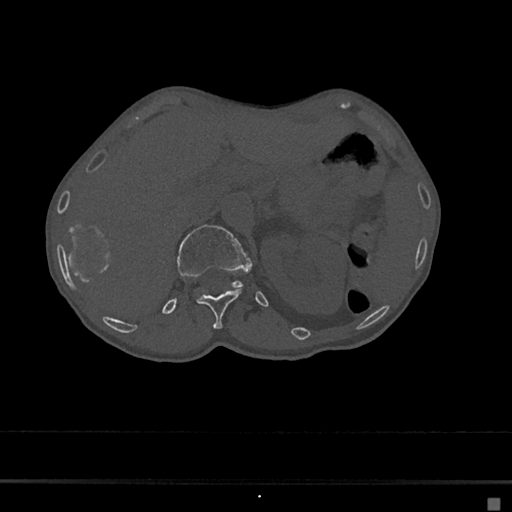
CT including the spine, one axial slice; reconstruction kernel Br40s/3; 120 kVp; bone window (W 1800 / L 400 HU); 0.5 mm slice thickness; 512 × 512 image matrix, field of view 360 × 360 mm. Patient: female, 68 years. Case-level facts recorded for this patient, not image findings: primary cancer: renal.
Structures marked on this image (semi-automatic segmentation, software-assisted and operator-edited):
- L1 vertebra: bounding box <176,225,252,288> (left, top, right, bottom; pixels)
- T12 vertebra: <197,291,240,329>